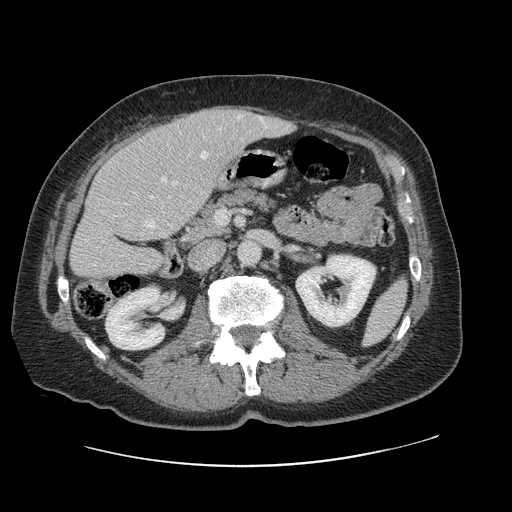
Contrast-enhanced abdominal CT, one axial slice. Position 42 of 138 along the scan axis. Intravenous contrast given. Soft-tissue window (W 400 / L 40 HU). 2.5 mm slice thickness. 512 × 512 image matrix, field of view 402 × 402 mm. Male patient, age 71 years. Case-level facts recorded for this patient, not image findings: diagnosis: colorectal cancer liver metastases, imaged before liver resection; multiple liver metastases: no; largest metastasis: 3.3 cm.
Annotated regions visible in this slice (expert manual segmentation):
- hepatic veins: box from (x=93, y=115) to (x=267, y=266) px
- liver: (x=72, y=107)–(x=292, y=279)
- planned liver remnant (the part of the liver to remain after resection): (x=72, y=136)–(x=193, y=280)
- portal vein (with intrahepatic branches): (x=162, y=178)–(x=166, y=182)